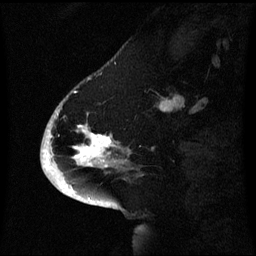
Breast MRI (dynamic contrast-enhanced), one sagittal slice; slice 20 of 60 in the series (ordered by position); dynamic contrast-enhanced series, image 2 of 3 at this slice position (ordered by acquisition); 1.5 T; TE 4.2 ms, TR 8.4 ms; 2.1 mm slice thickness; 256 × 256 image matrix, field of view 220 × 220 mm. Female patient, age 53 years. Case-level facts recorded for this patient, not image findings: setting: breast cancer imaged before/during neoadjuvant chemotherapy; receptor status: HR-positive, HER2-negative.
Annotated regions visible in this slice (semi-automatic segmentation, software-assisted and operator-edited):
- analysis volume of interest (the breast-tissue region the enhancement analysis was run in; not a lesion): bounding box <52,90,131,171> (left, top, right, bottom; pixels)
- tumour enhancement mask (voxels above the 70 % enhancement threshold inside the analysis volume of interest): <75,126,112,165>